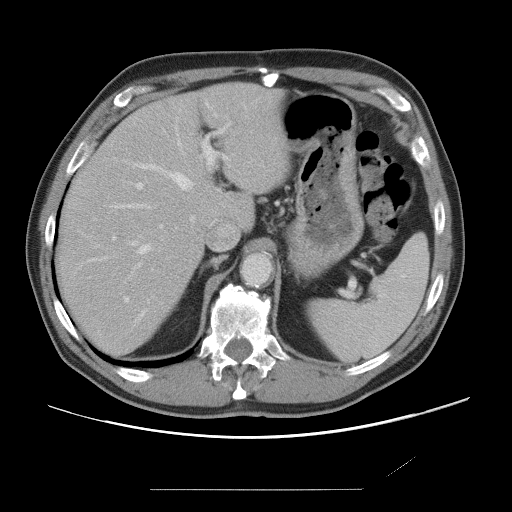
Contrast-enhanced abdominal CT, one axial slice. Position 51 of 87 along the scan axis. Soft-tissue window (W 400 / L 40 HU). 5 mm slice thickness. 512 × 512 image matrix, field of view 406 × 406 mm. Male patient, age 74 years. Case-level facts recorded for this patient, not image findings: diagnosis: colorectal cancer liver metastases, imaged before liver resection; multiple liver metastases: yes; largest metastasis: 1.1 cm; disease in both lobes: no.
Structures marked on this image (manually delineated by an expert):
- hepatic veins: bounding box [x1, y1, x2, y2] px = [117, 107, 246, 317]
- liver: [59, 84, 287, 356]
- planned liver remnant (the part of the liver to remain after resection): [59, 84, 286, 356]
- portal vein (with intrahepatic branches): [112, 124, 230, 302]